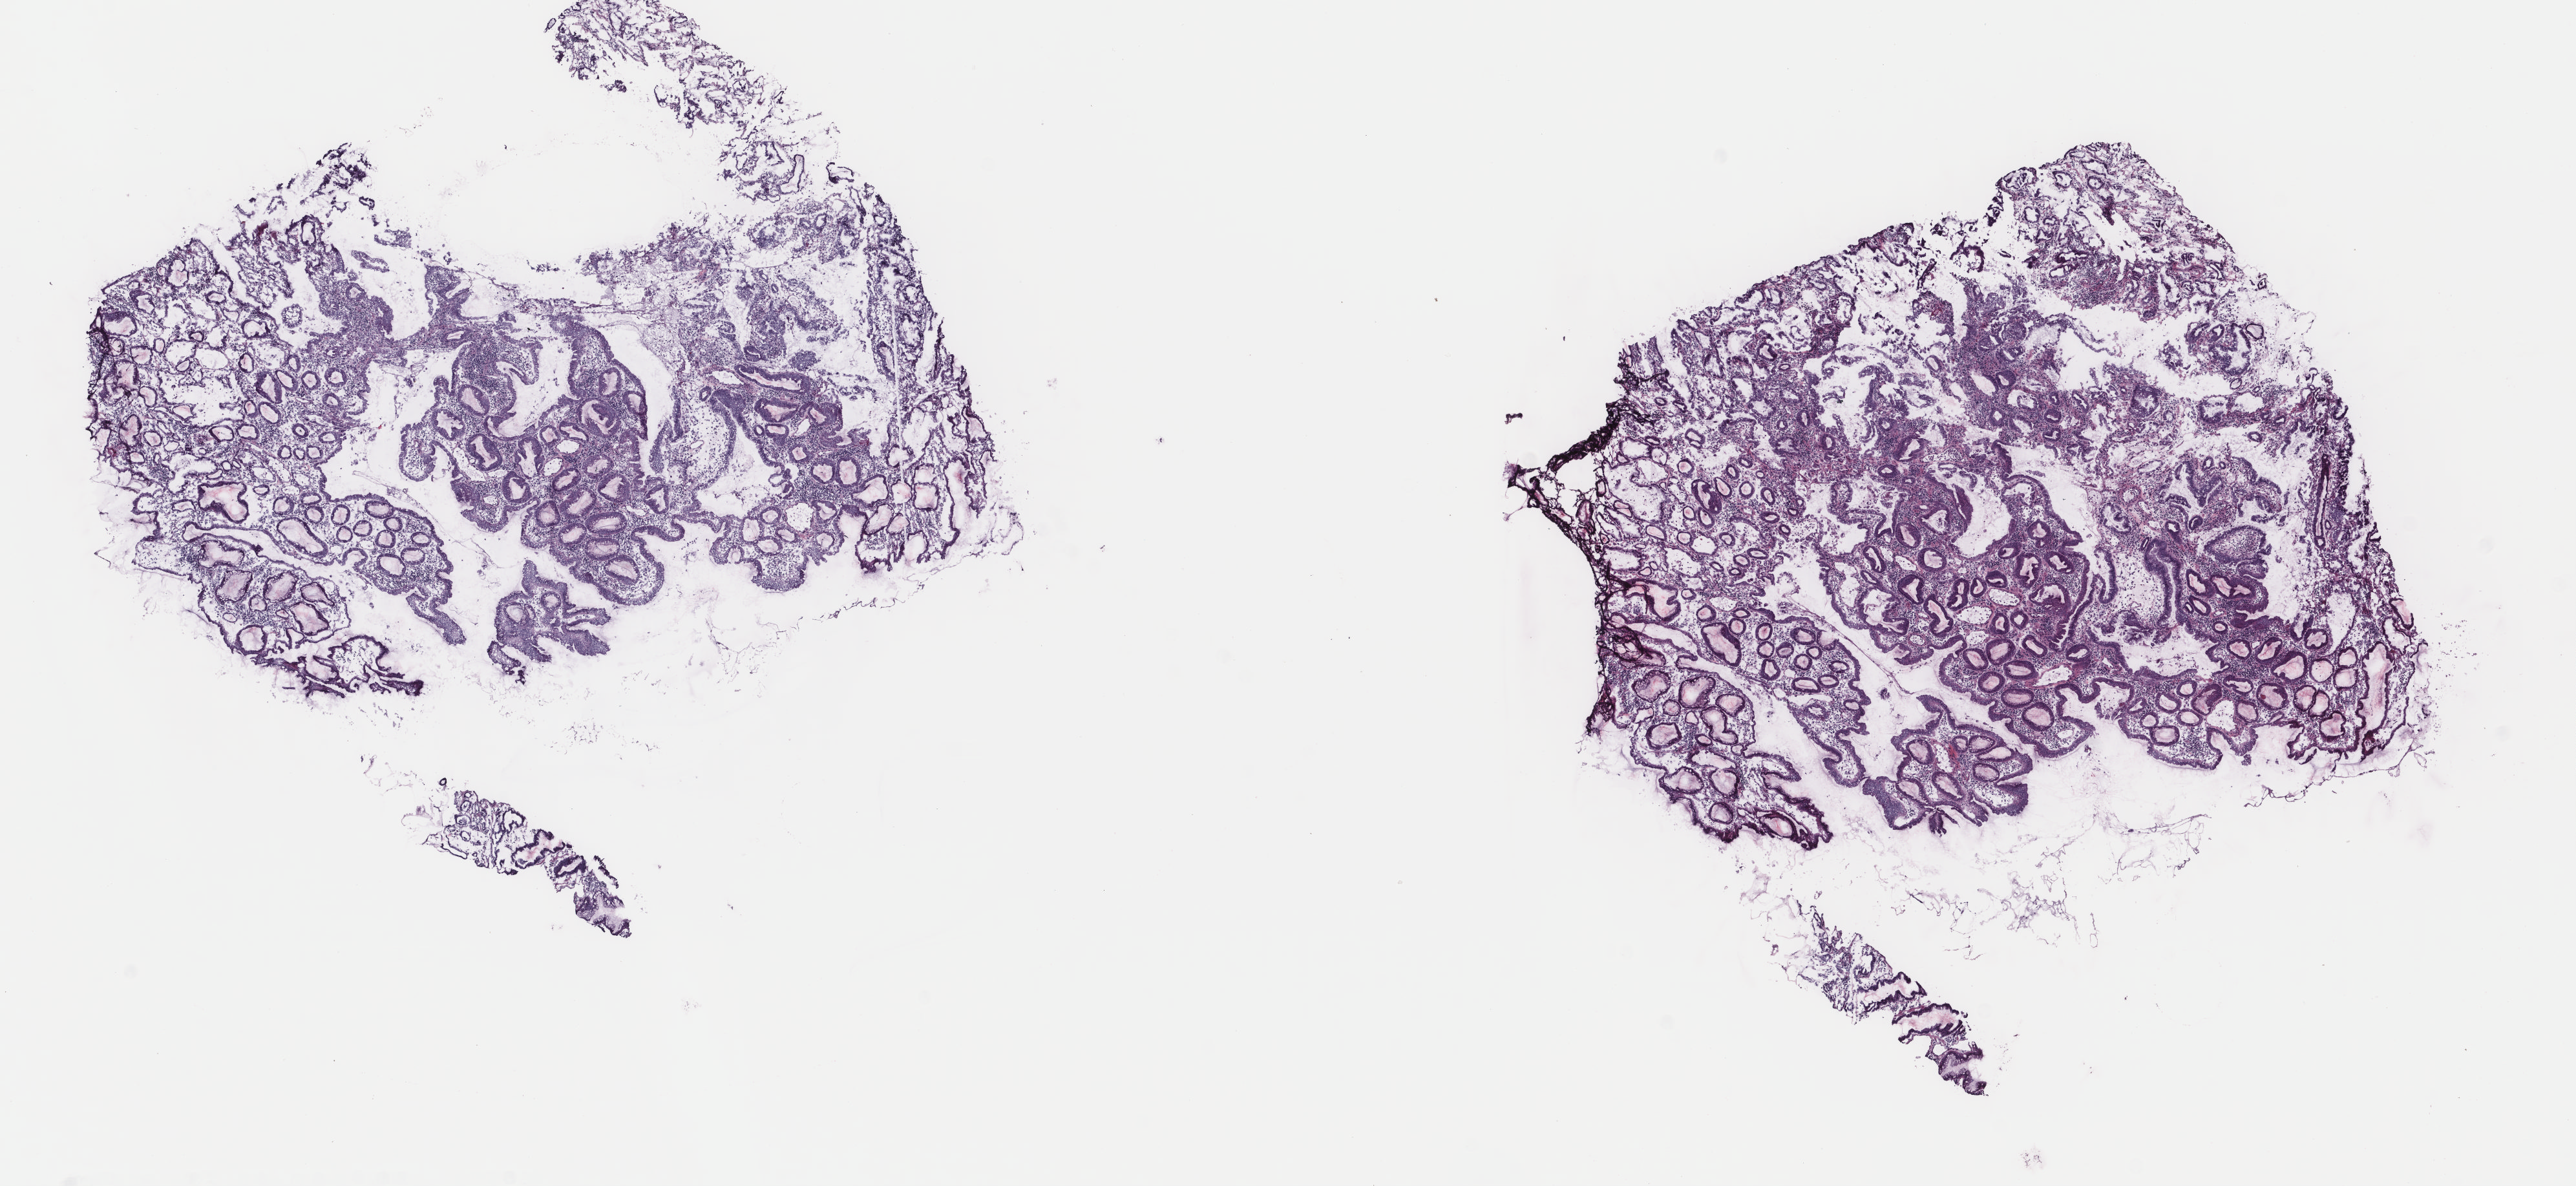
Whole-slide histology image, H&E-stained — shown as a low-resolution overview of the whole scanned area (about 15.8 x 7.3 mm, from a 40x scan). Frozen section. Esophagus, primary tumour sample. Female, age 84 years at initial diagnosis. Histologic grade: GX (grade cannot be assessed). Pathologist review of this section (percent, as recorded): tumour cells 100%, tumour nuclei 85%, normal cells 0%, stromal cells 0%, necrosis 0%. Inflammatory infiltration, as recorded: lymphocyte infiltration 2%, monocyte infiltration 1%, neutrophil infiltration 1%.
Pathologic diagnosis: Adenocarcinoma, NOS.